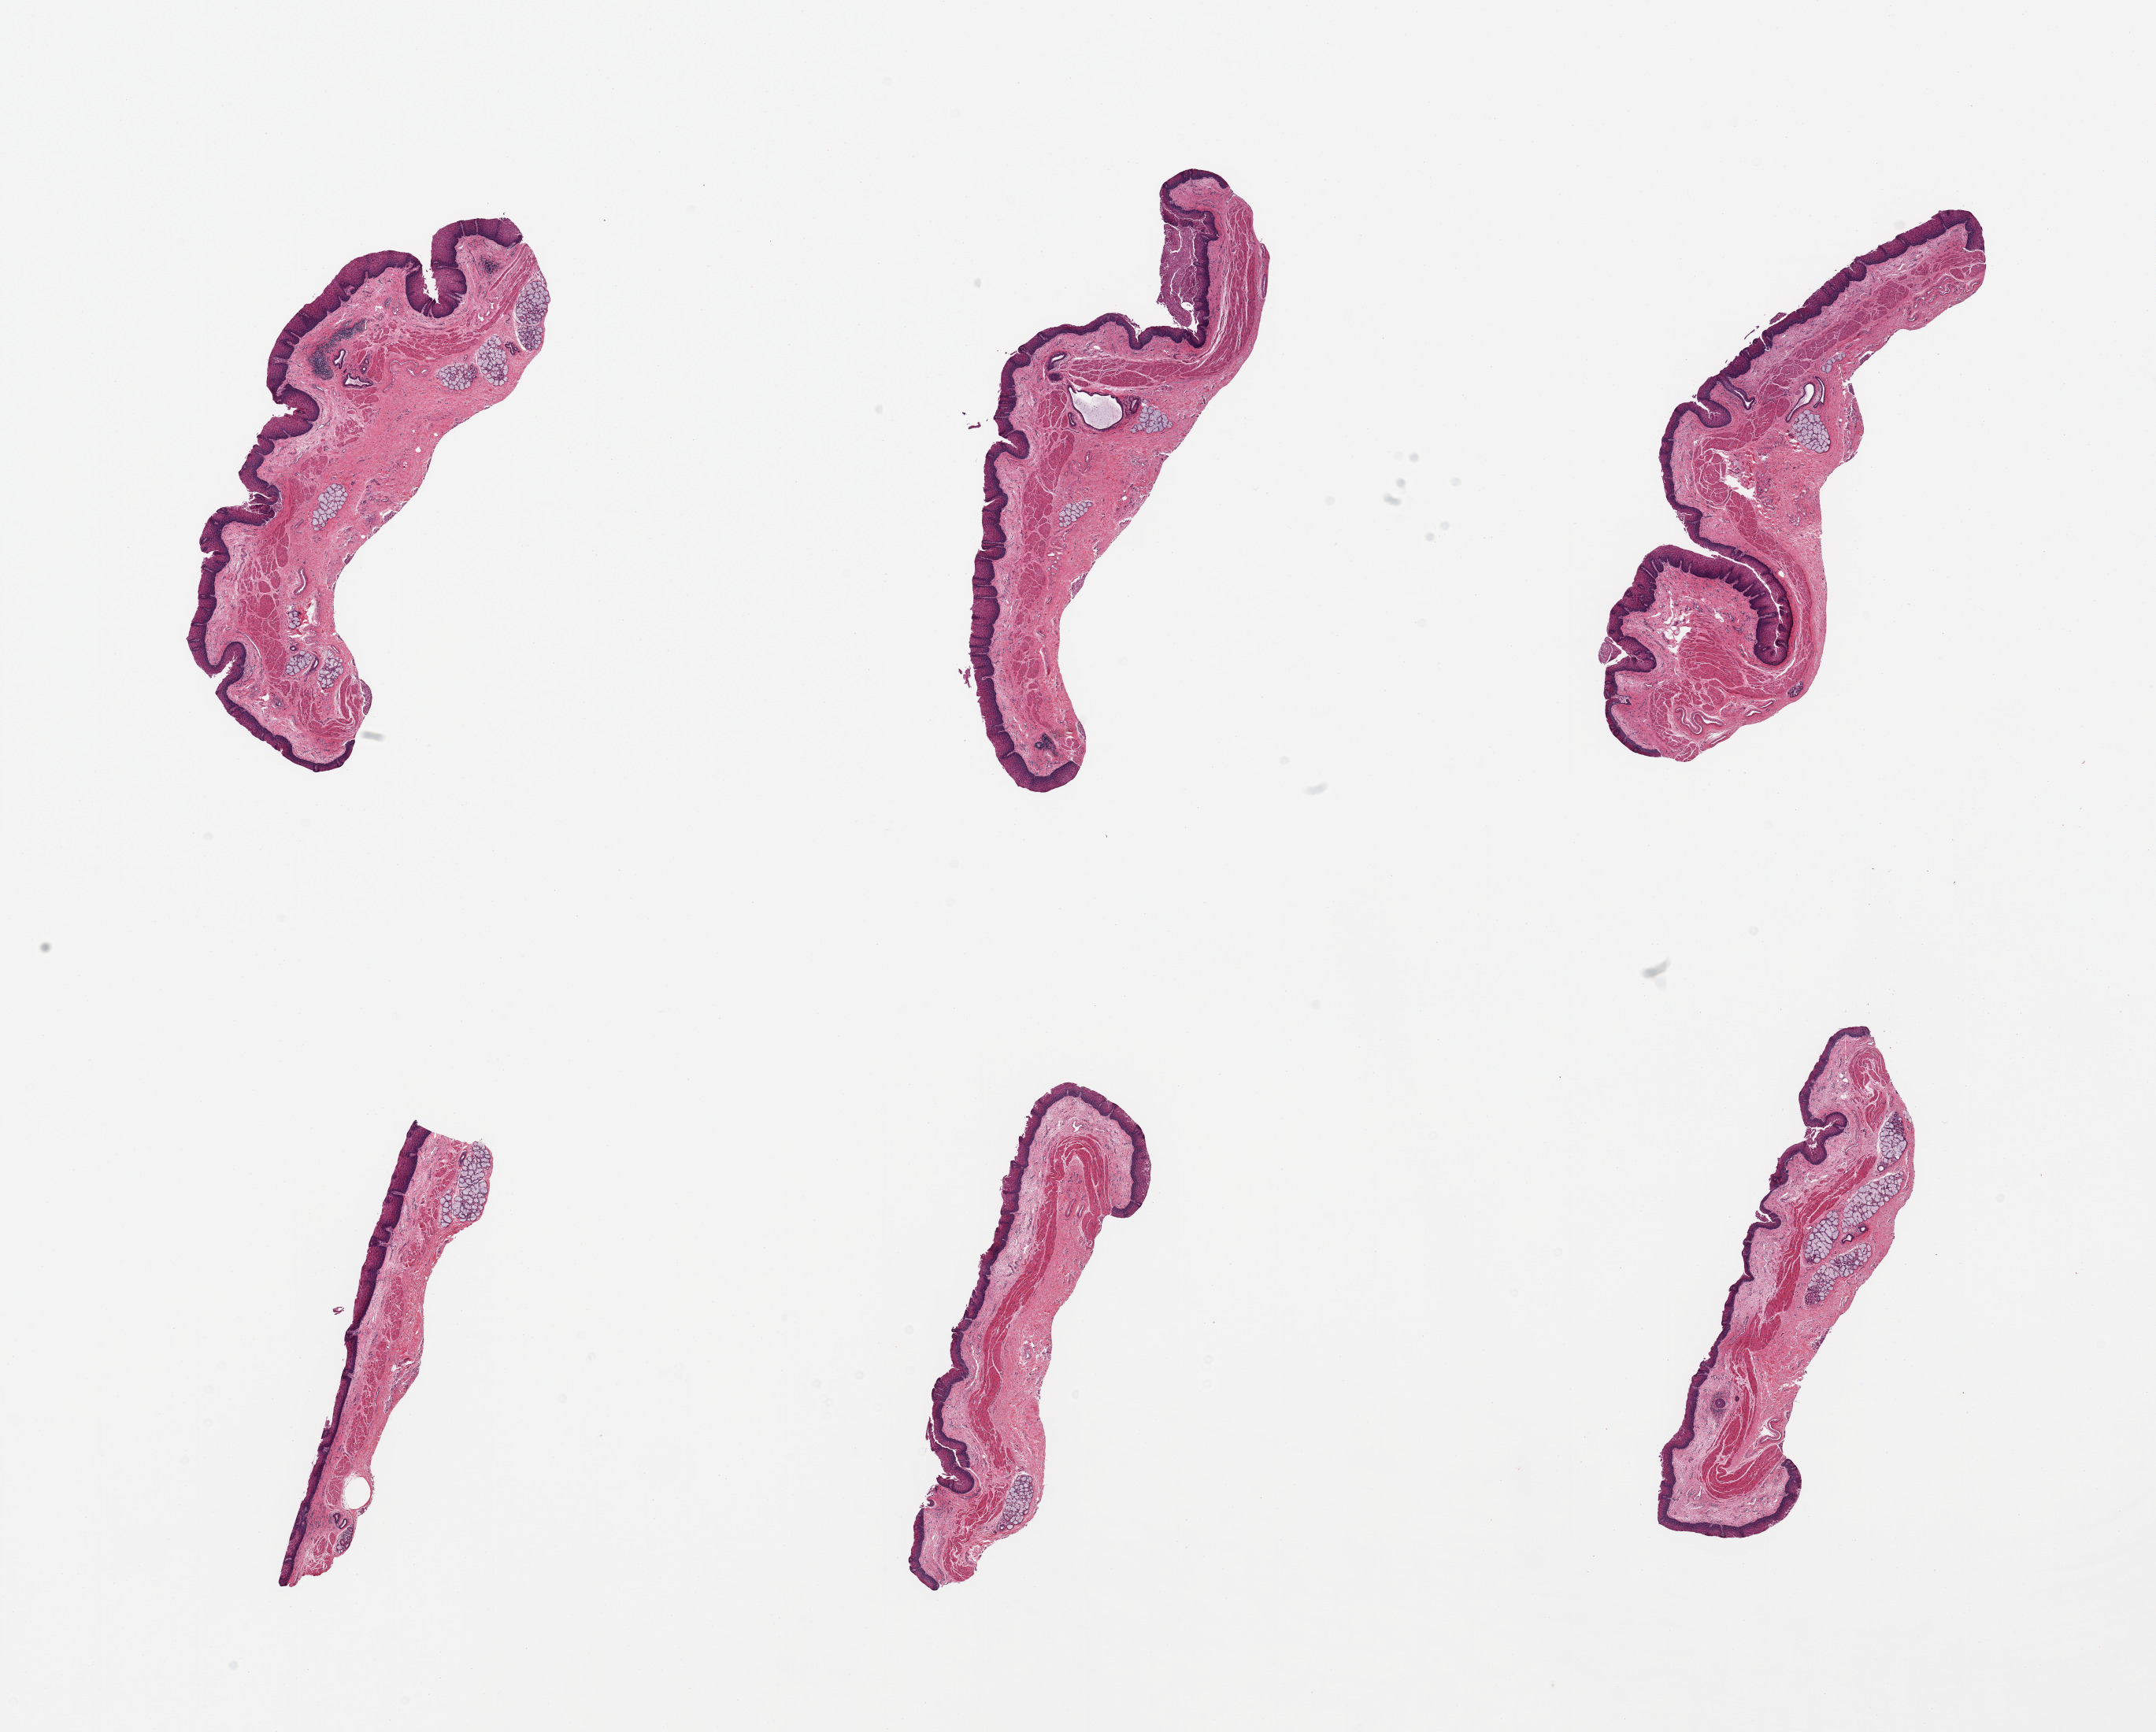
Digitized haematoxylin and eosin-stained section, shown as a low-resolution overview of the whole scanned area (about 21.7 x 17.4 mm, from a 20x scan); PAXgene-fixed paraffin-embedded (PFPE) section; target tissue: esophageal mucous membrane; tissue donor sample. Donor sex: male.
Reviewer comment on this tissue sample: 6 pieces; submucosal glands comprise up to 10%; well dissected.